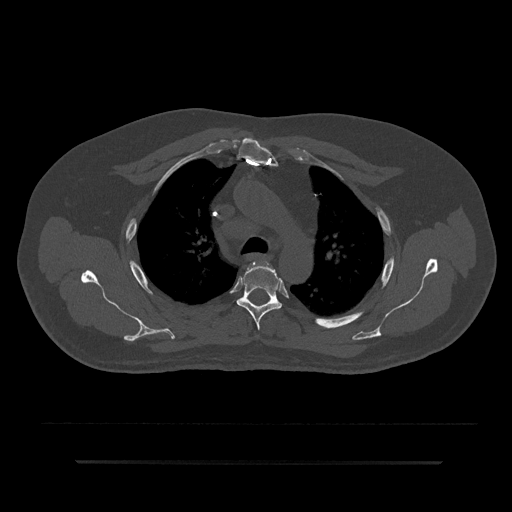
CT including the spine, one axial slice; position 617 of 797 along the scan axis; reconstruction kernel Br40s/3; bone window (W 1800 / L 400 HU); 0.5 mm slice thickness; 512 × 512 image matrix. Male patient, age 59 years. Case-level facts recorded for this patient, not image findings: primary cancer: bile ducts.
Outlined on this slice (semi-automatic segmentation, software-assisted and operator-edited):
- T3 vertebra: box from (x=257, y=262) to (x=273, y=269) px
- T4 vertebra: (x=231, y=262)–(x=282, y=330)
- T5 vertebra: (x=245, y=297)–(x=271, y=303)